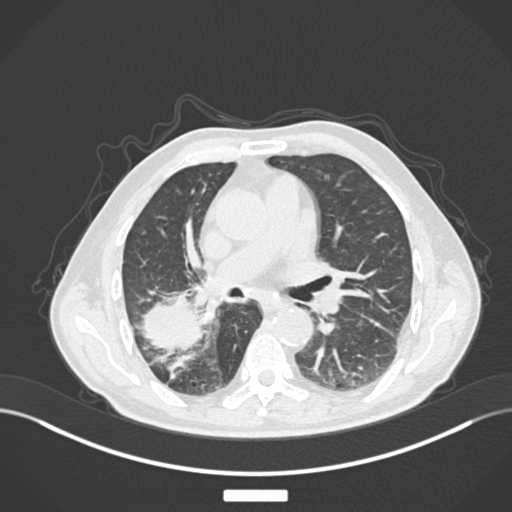
Chest CT, one axial slice. Position 94 of 201 along the scan axis. Reconstruction kernel B30f. 120 kVp. Lung window (W 1500 / L -600 HU). 1 mm slice thickness. 512 × 512 image matrix, field of view 400 × 400 mm. Male patient, age 72 years. From the clinical record (not read from this slice): clinical TNM (as recorded): T3 N2 M0.
Annotated regions visible in this slice (rectangle marked by the reading radiologist):
- lung tumour (recorded histology: adenocarcinoma): bounding box (x1, y1, x2, y2) in pixels: (139, 295, 204, 355)